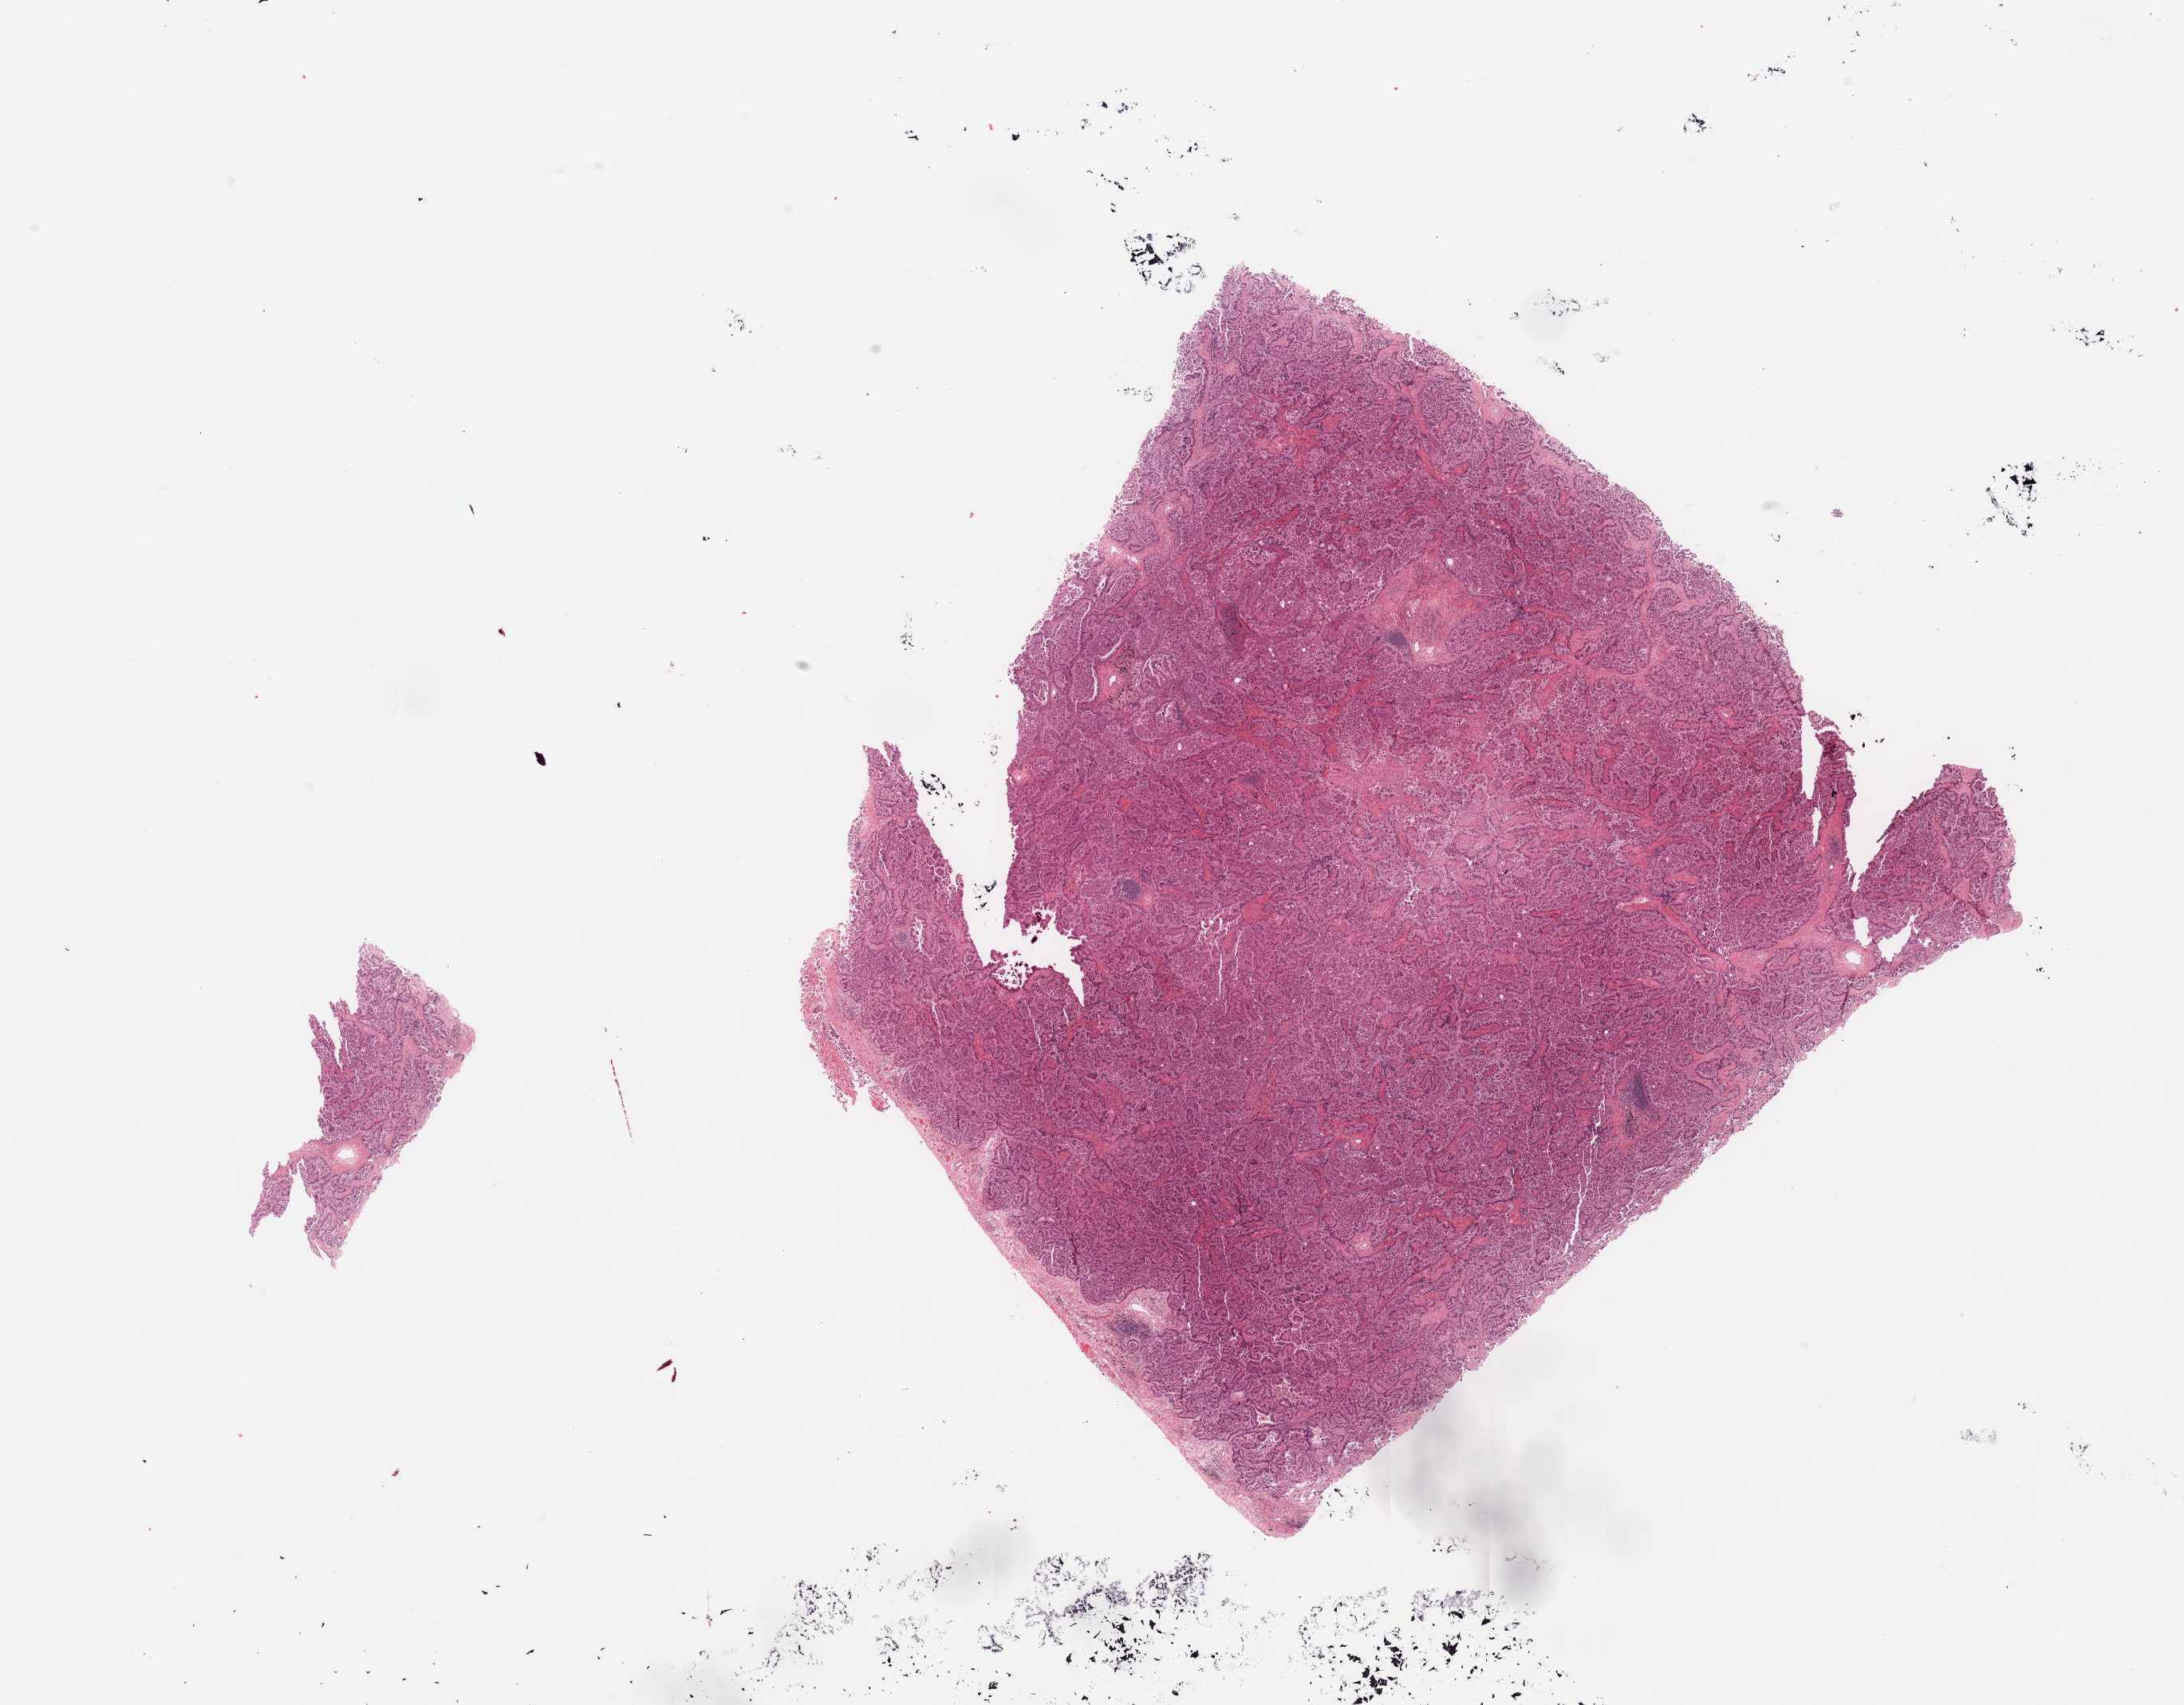
Whole-slide histology image, Hematoxylin and eosin (H&E) stained, a low-resolution overview of the entire scanned area, about 21.7 x 16.9 mm; tumour tissue sample, sampled site: lung. Patient: male, age 45 years. Histologic grade: G3 (poorly differentiated). Slide review estimates, as recorded: tumour nuclei 85%, necrosis 0%.
• primary tumour site (as recorded): left upper lobe
• AJCC pathologic stage: IB
• diagnosis: Adenocarcinoma, NOS